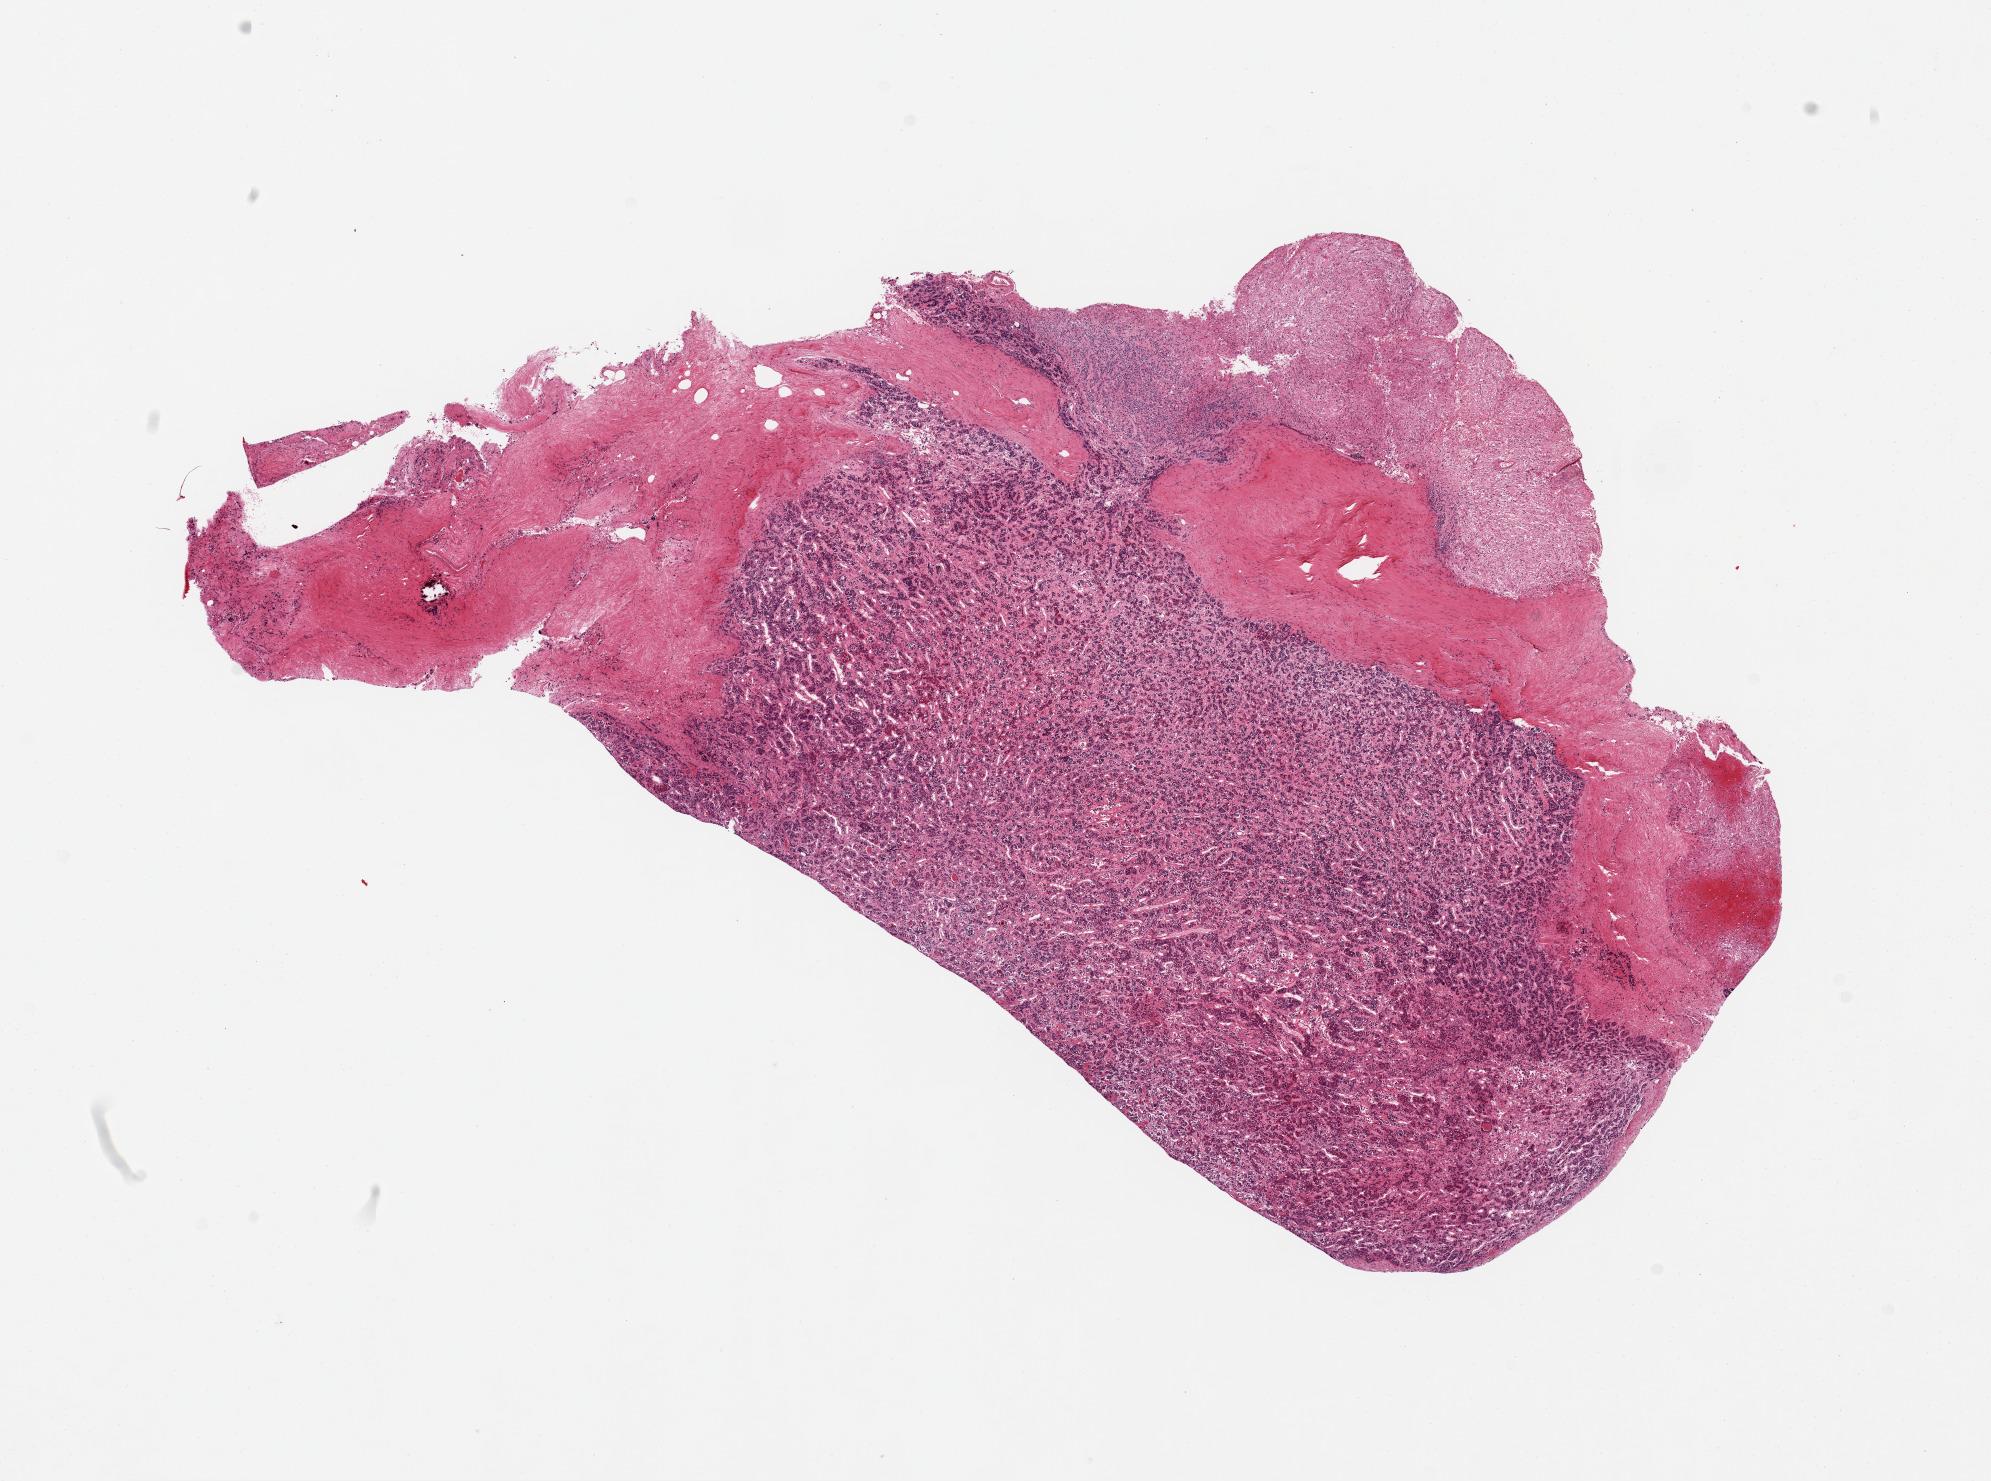
Whole-slide image, H&E stain — a low-resolution overview of the entire scanned area, about 15.8 x 11.7 mm, PAXgene-fixed paraffin-embedded (PFPE) section, sampled site (target tissue): pituitary, donor tissue sample. Male donor.
Pathologist's review note for this sample: 1 piece; not cerebellum, pituitary, adenohypophysis and neurohypophysis, portion of dura.